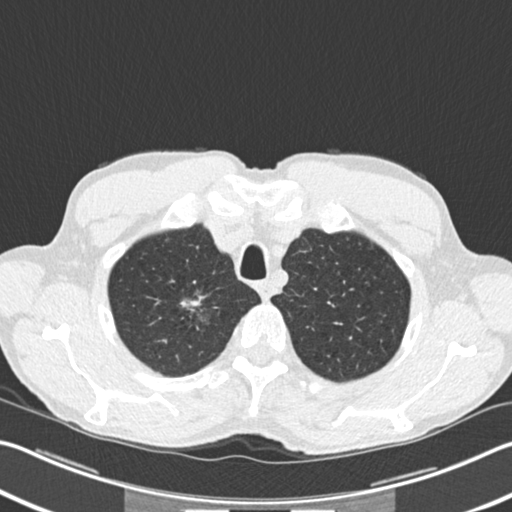
Axial slice from a low-dose chest CT screening exam. Second annual screen. Lung window (W 1500 / L -600 HU). 2 mm slice thickness. Standard (soft-tissue) reconstruction kernel (B30f). 120 kVp. Slice 32 of 220 in the series. Male, age 62 years at enrolment. Former smoker at enrolment.
Expert-annotated lung lesion, bounding box (x1, y1, x2, y2) in pixels: (173, 288, 215, 336). The screening reader recorded 2 non-calcified nodules or masses ≥4 mm on this exam; which of them this box marks is not recorded. Lung cancer was diagnosed 5 days after this screen: bronchiolo-alveolar adenocarcinoma, NOS, right upper lobe, well differentiated (G1), stage IA (AJCC 6th edition), 15 mm at pathology.